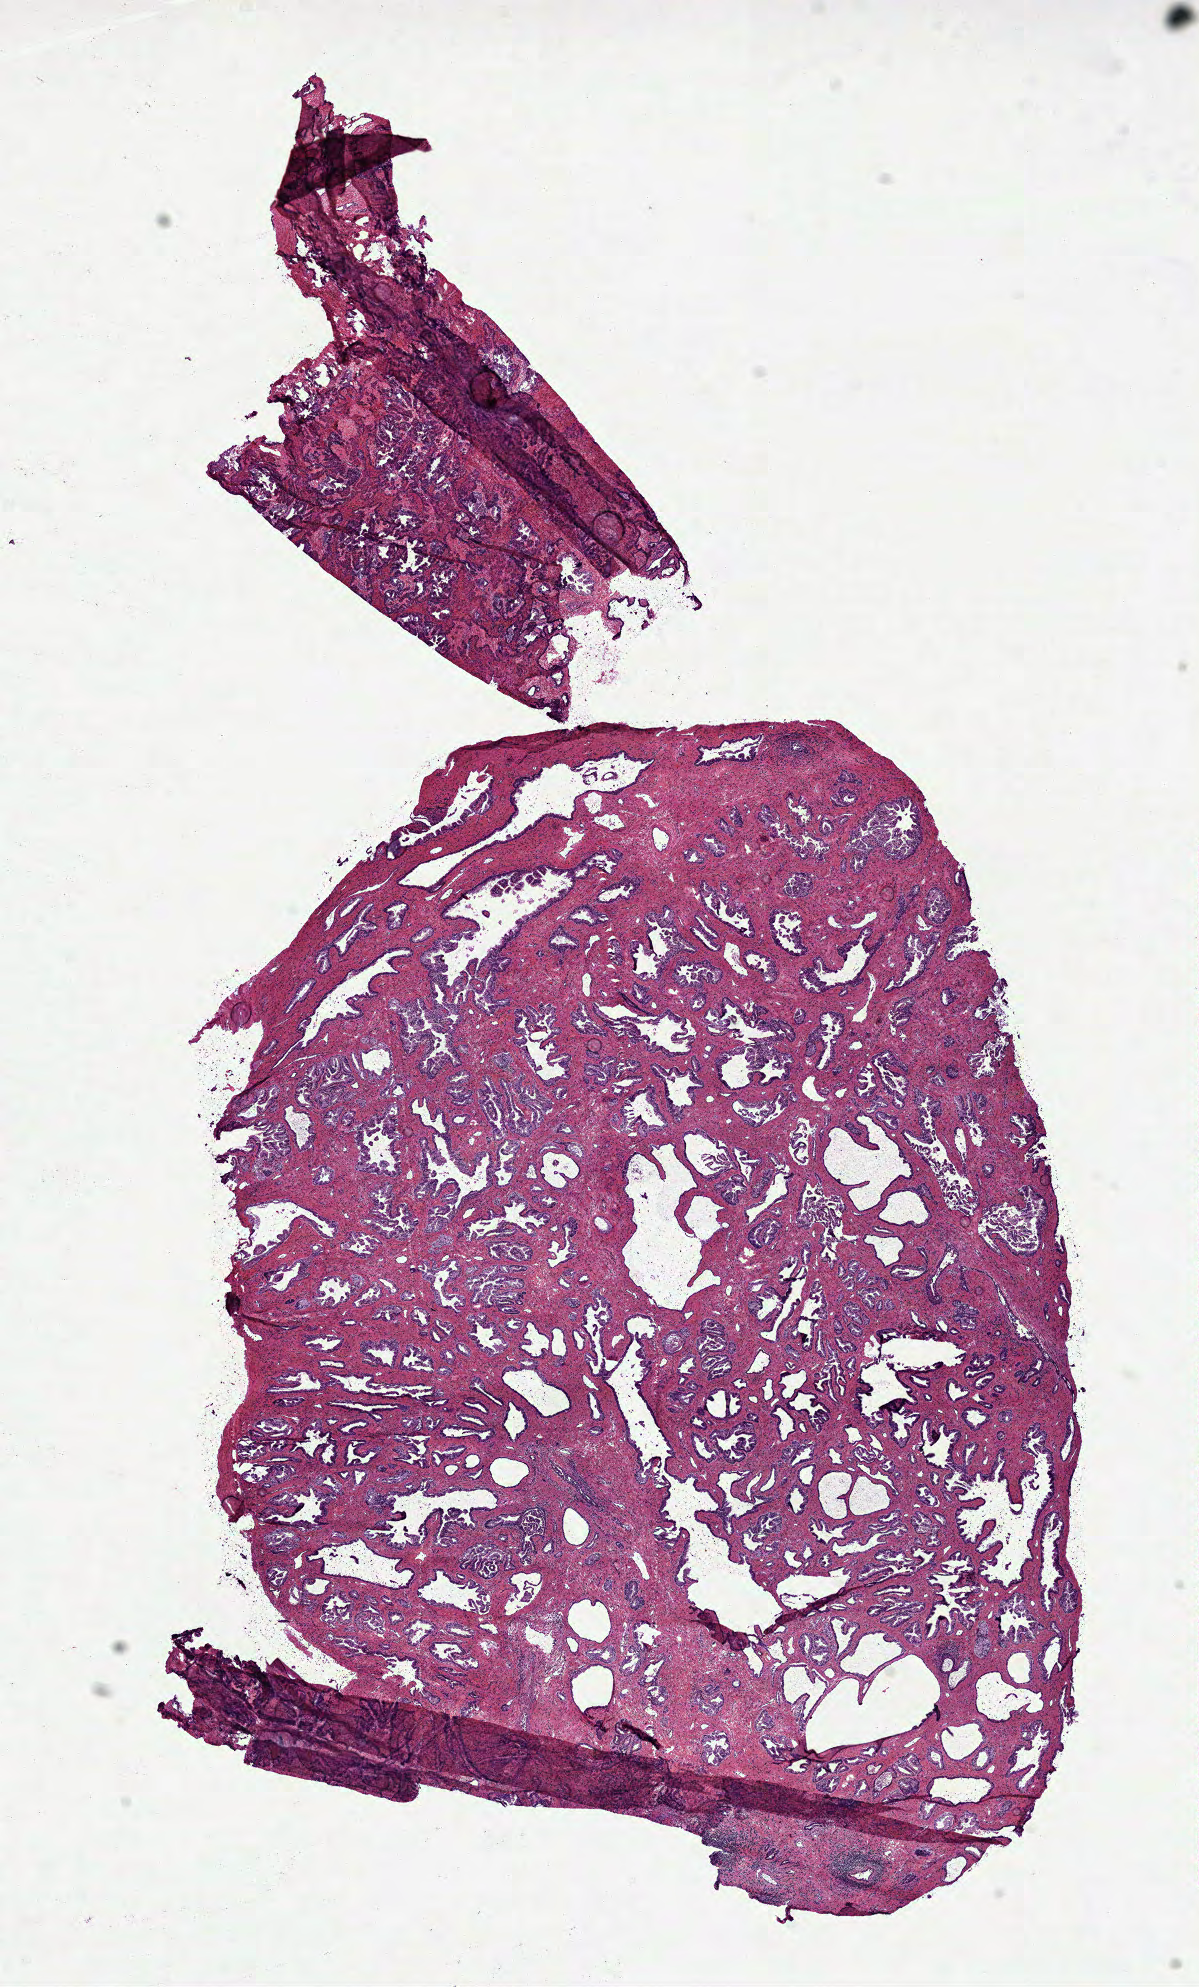
Digitized H&E tissue section (whole slide) — whole scanned area (about 9.7 x 16.0 mm, acquisition: 40x scan) shown as a low-resolution overview, frozen section from the top of the tissue portion, prostate, solid tissue normal (non-tumour tissue) sample. Male patient; age at initial diagnosis 71 years.
- this section: solid tissue normal (non-tumour) sample from the same patient
- patient diagnosis: Acinar cell carcinoma (prostate gland)